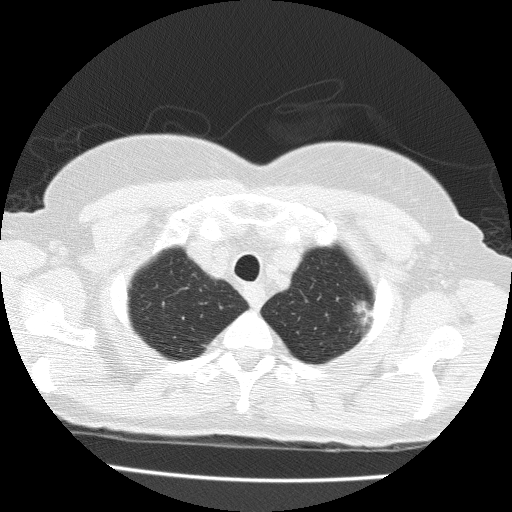
Chest CT (low-dose screening protocol), one axial image. Baseline screening round. Lung window (W 1500 / L -600 HU). 2 mm slice thickness. 120 kVp. Slice 22 of 183 in the series. 512 × 512 image matrix, field of view 320 × 320 mm. Female participant, aged 71 years at enrolment.
- Lesion marked by an expert reader, bounding box <340,292,386,333> (left, top, right, bottom; pixels).
- The exam's reader record, not a measurement of the box and not confirmed to be the same lesion: non-calcified nodule or mass ≥4 mm, left upper lobe, 15 × 10 mm, spiculated (stellate) margins, soft tissue attenuation.
- Official screen result: positive, change unspecified: nodule(s) >= 4 mm or enlarging nodule(s), mass(es), or other non-specific abnormalities suspicious for lung cancer.
- Lung cancer was diagnosed 49 days after this screen: adenocarcinoma with mixed subtypes, left upper lobe, well differentiated (G1), stage IA (AJCC 6th edition), 15 mm at pathology.